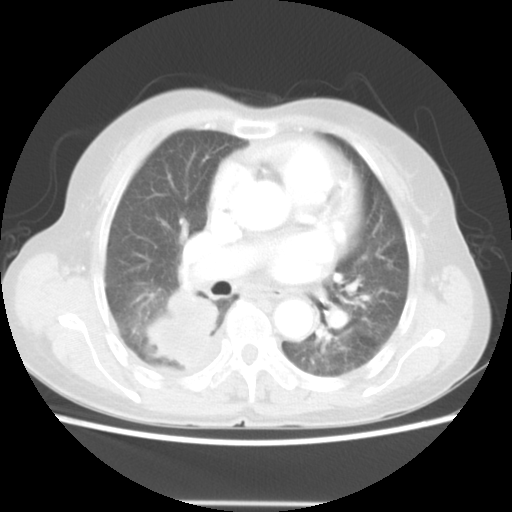
Chest CT, one axial slice; position 28 of 52 along the scan axis; reconstruction kernel STANDARD; lung window (W 1500 / L -600 HU); 5 mm slice thickness; 512 × 512 image matrix. Female patient, age 67 years. Case-level facts recorded for this patient, not image findings: clinical TNM (as recorded): T3 N1 M1.
Outlined on this slice (bounding box drawn by a radiologist):
- lung tumour (recorded histology: adenocarcinoma): box from (x=145, y=283) to (x=220, y=367) px